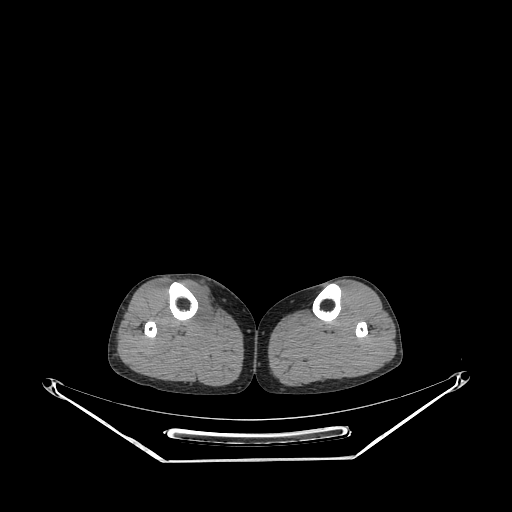
CT of an extremity soft-tissue mass (from a PET/CT study), one axial slice; reconstruction kernel STANDARD; soft-tissue window (W 400 / L 40 HU); 3.75 mm slice thickness; 512 × 512 image matrix, field of view 500 × 500 mm. Female patient. Case-level facts recorded for this patient, not image findings: histological type: undifferentiated – high grade; grade: high; site of the primary tumour: right thigh.
Outlined on this slice (expert contour drawn on MRI and transferred to this co-registered scan by the dataset authors):
- gross tumour volume (mass): box from (x=181, y=281) to (x=213, y=318) px